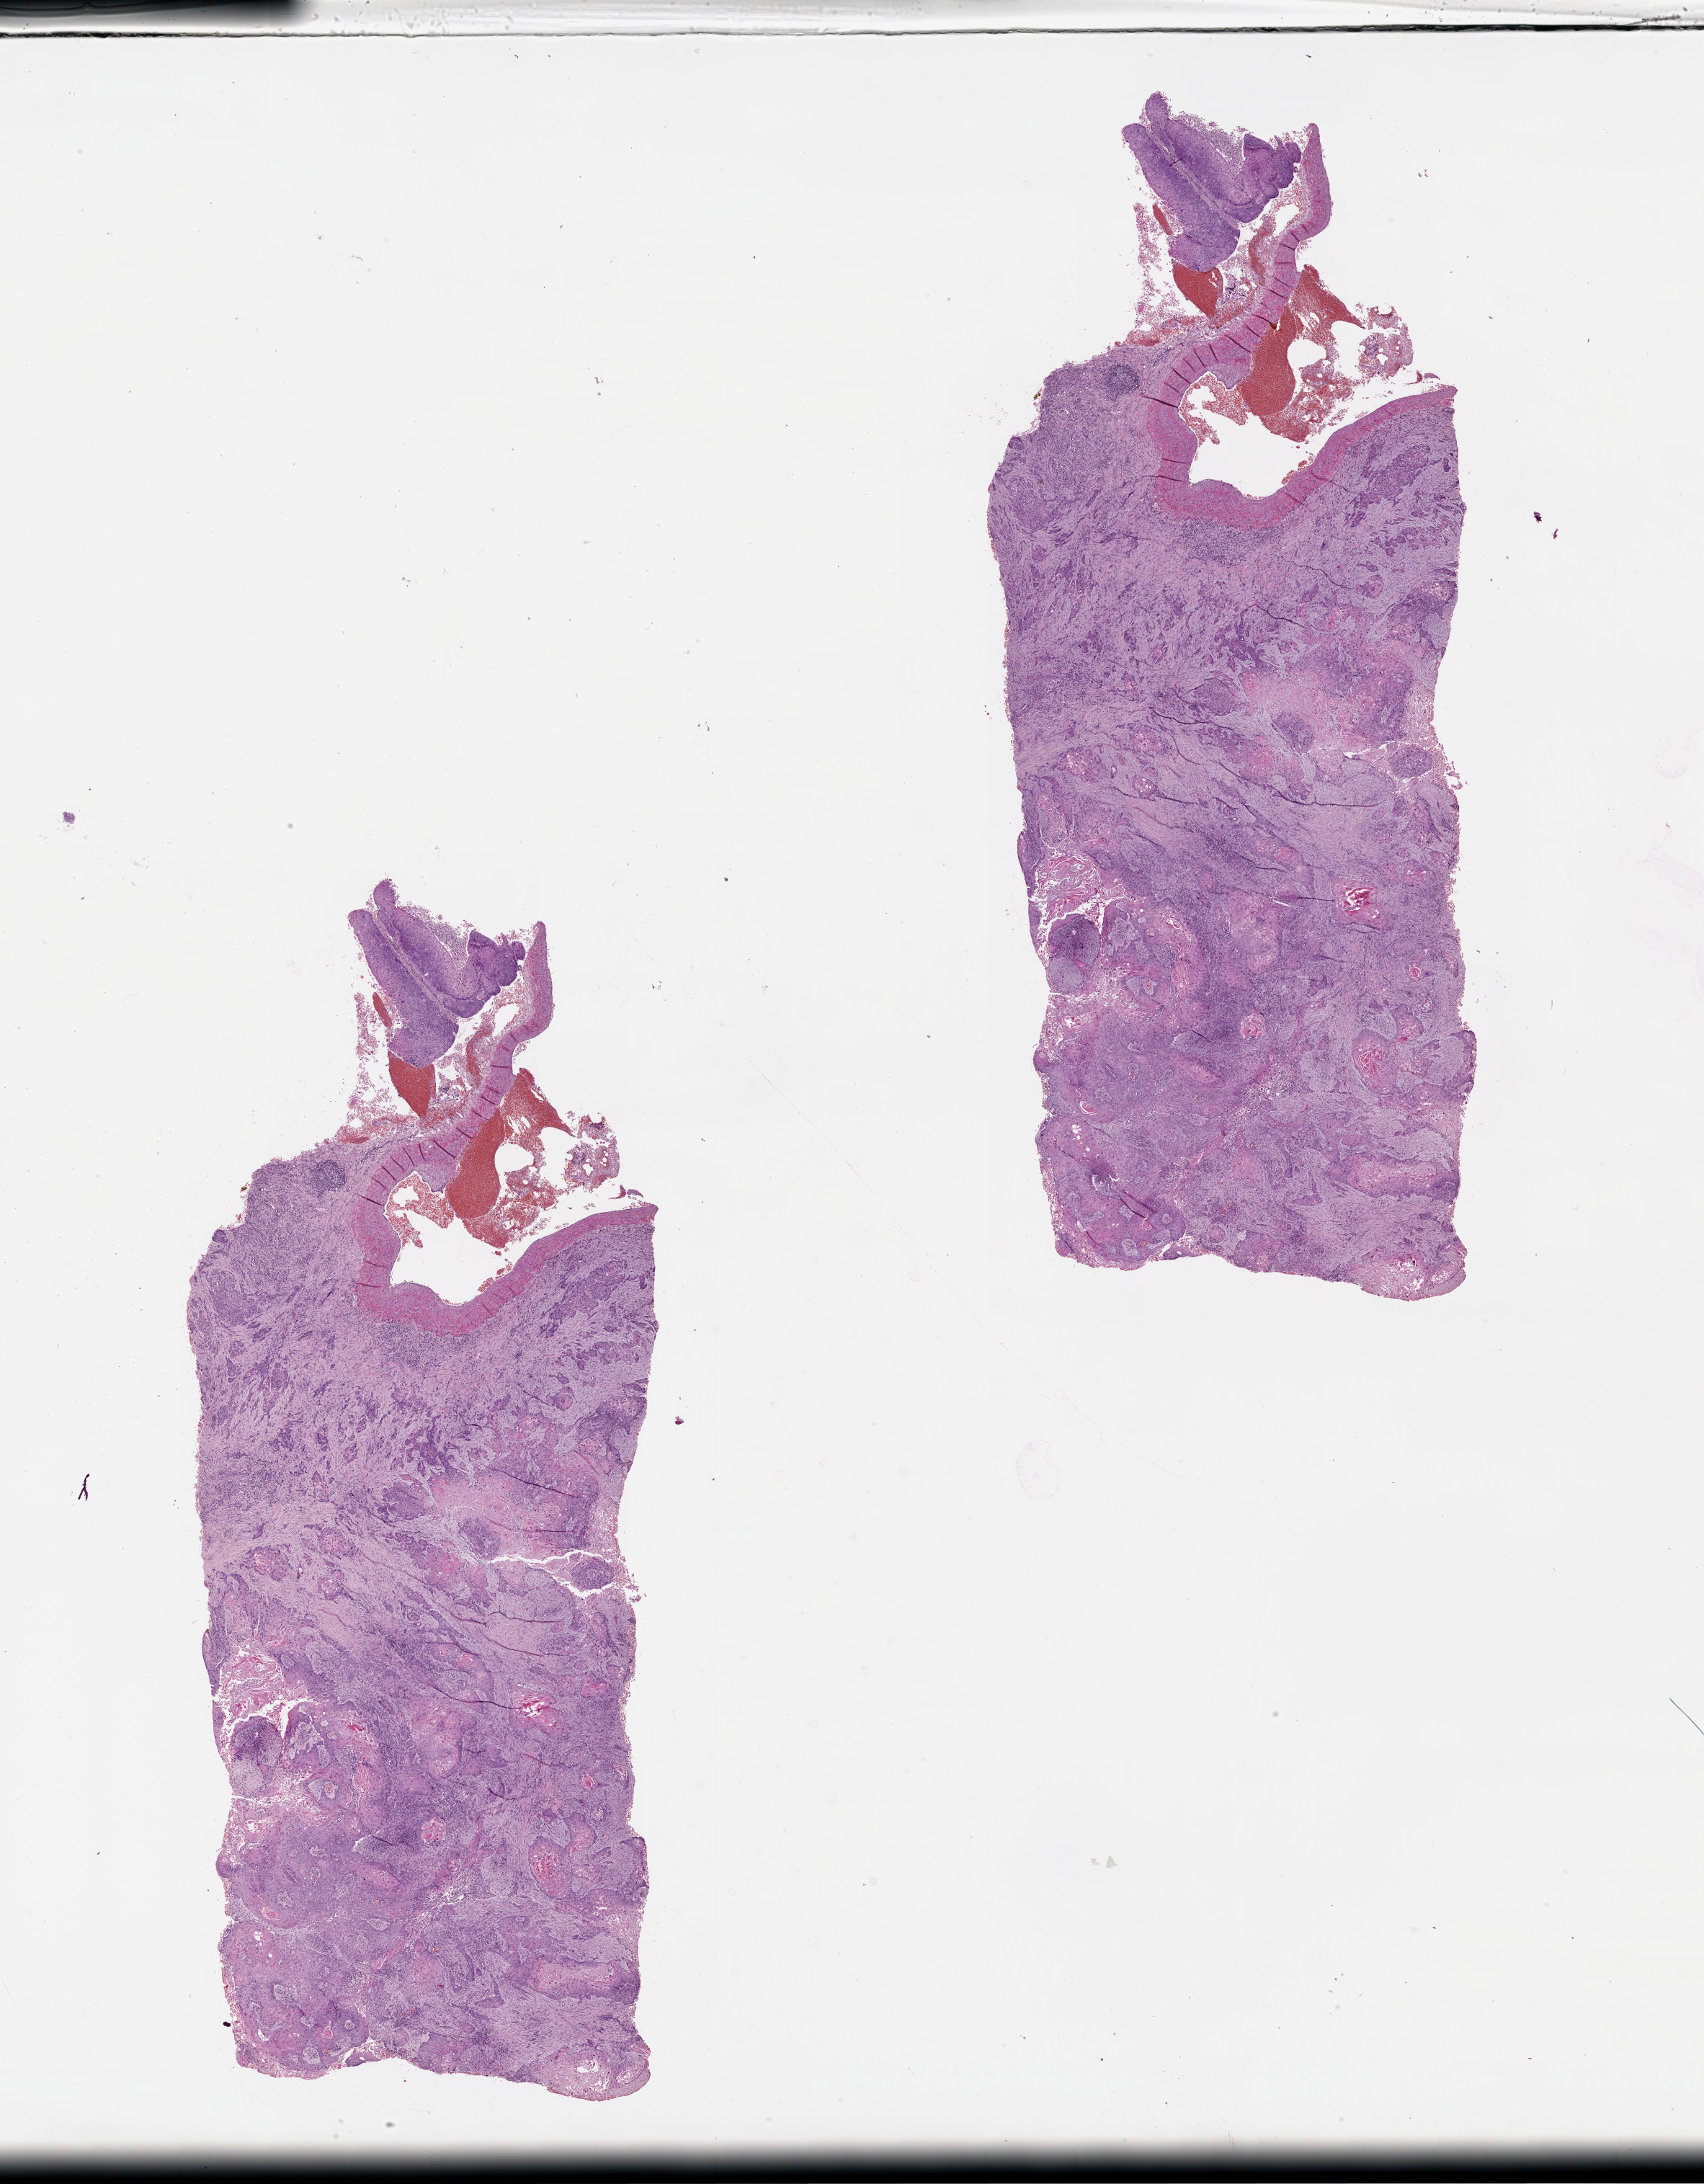
Whole-slide histology image, H&E-stained, whole scanned area (about 19.0 x 24.4 mm, slide scanned at 20x) shown as a low-resolution overview, lung, tumour tissue. Patient: female, age 60 years.
Patient diagnosis (cohort enrolment): squamous cell carcinoma (lung).